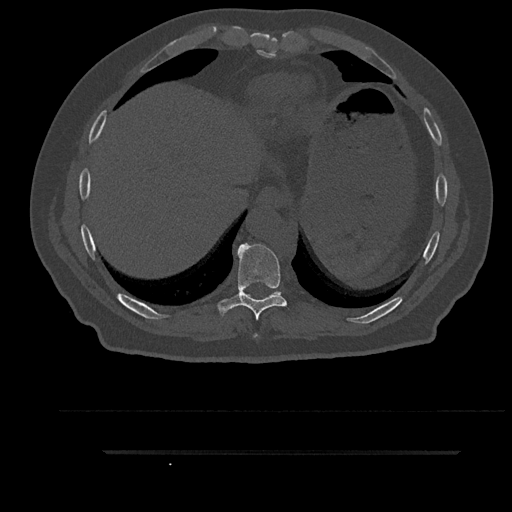
CT including the spine, one axial slice. Bone window (W 1800 / L 400 HU). 0.5 mm slice thickness. 512 × 512 image matrix. Male patient, age 63 years. From the clinical record (not read from this slice): primary cancer: renal.
Structures marked on this image (semi-automatic segmentation, software-assisted and operator-edited):
- T8 vertebra: bounding box <254,334,258,337> (left, top, right, bottom; pixels)
- T9 vertebra: <217,243,294,320>